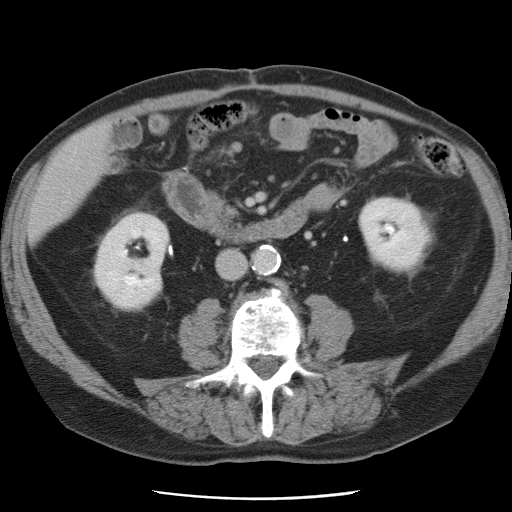
Contrast-enhanced abdominal CT, one axial slice; slice 17 of 78 in the series (ordered by position); 120 kVp; intravenous contrast given; soft-tissue window (W 400 / L 40 HU); 5 mm slice thickness; 512 × 512 image matrix, field of view 337 × 337 mm. Male patient, age 75 years. Case-level facts recorded for this patient, not image findings: diagnosis: colorectal cancer liver metastases, imaged before liver resection; multiple liver metastases: yes; largest metastasis: 2.4 cm; disease in both lobes: yes.
Annotated regions visible in this slice (outlined manually by an expert reader):
- liver: bounding box (x1, y1, x2, y2) in pixels: (32, 128, 108, 236)
- planned liver remnant (the part of the liver to remain after resection): (31, 128, 108, 237)